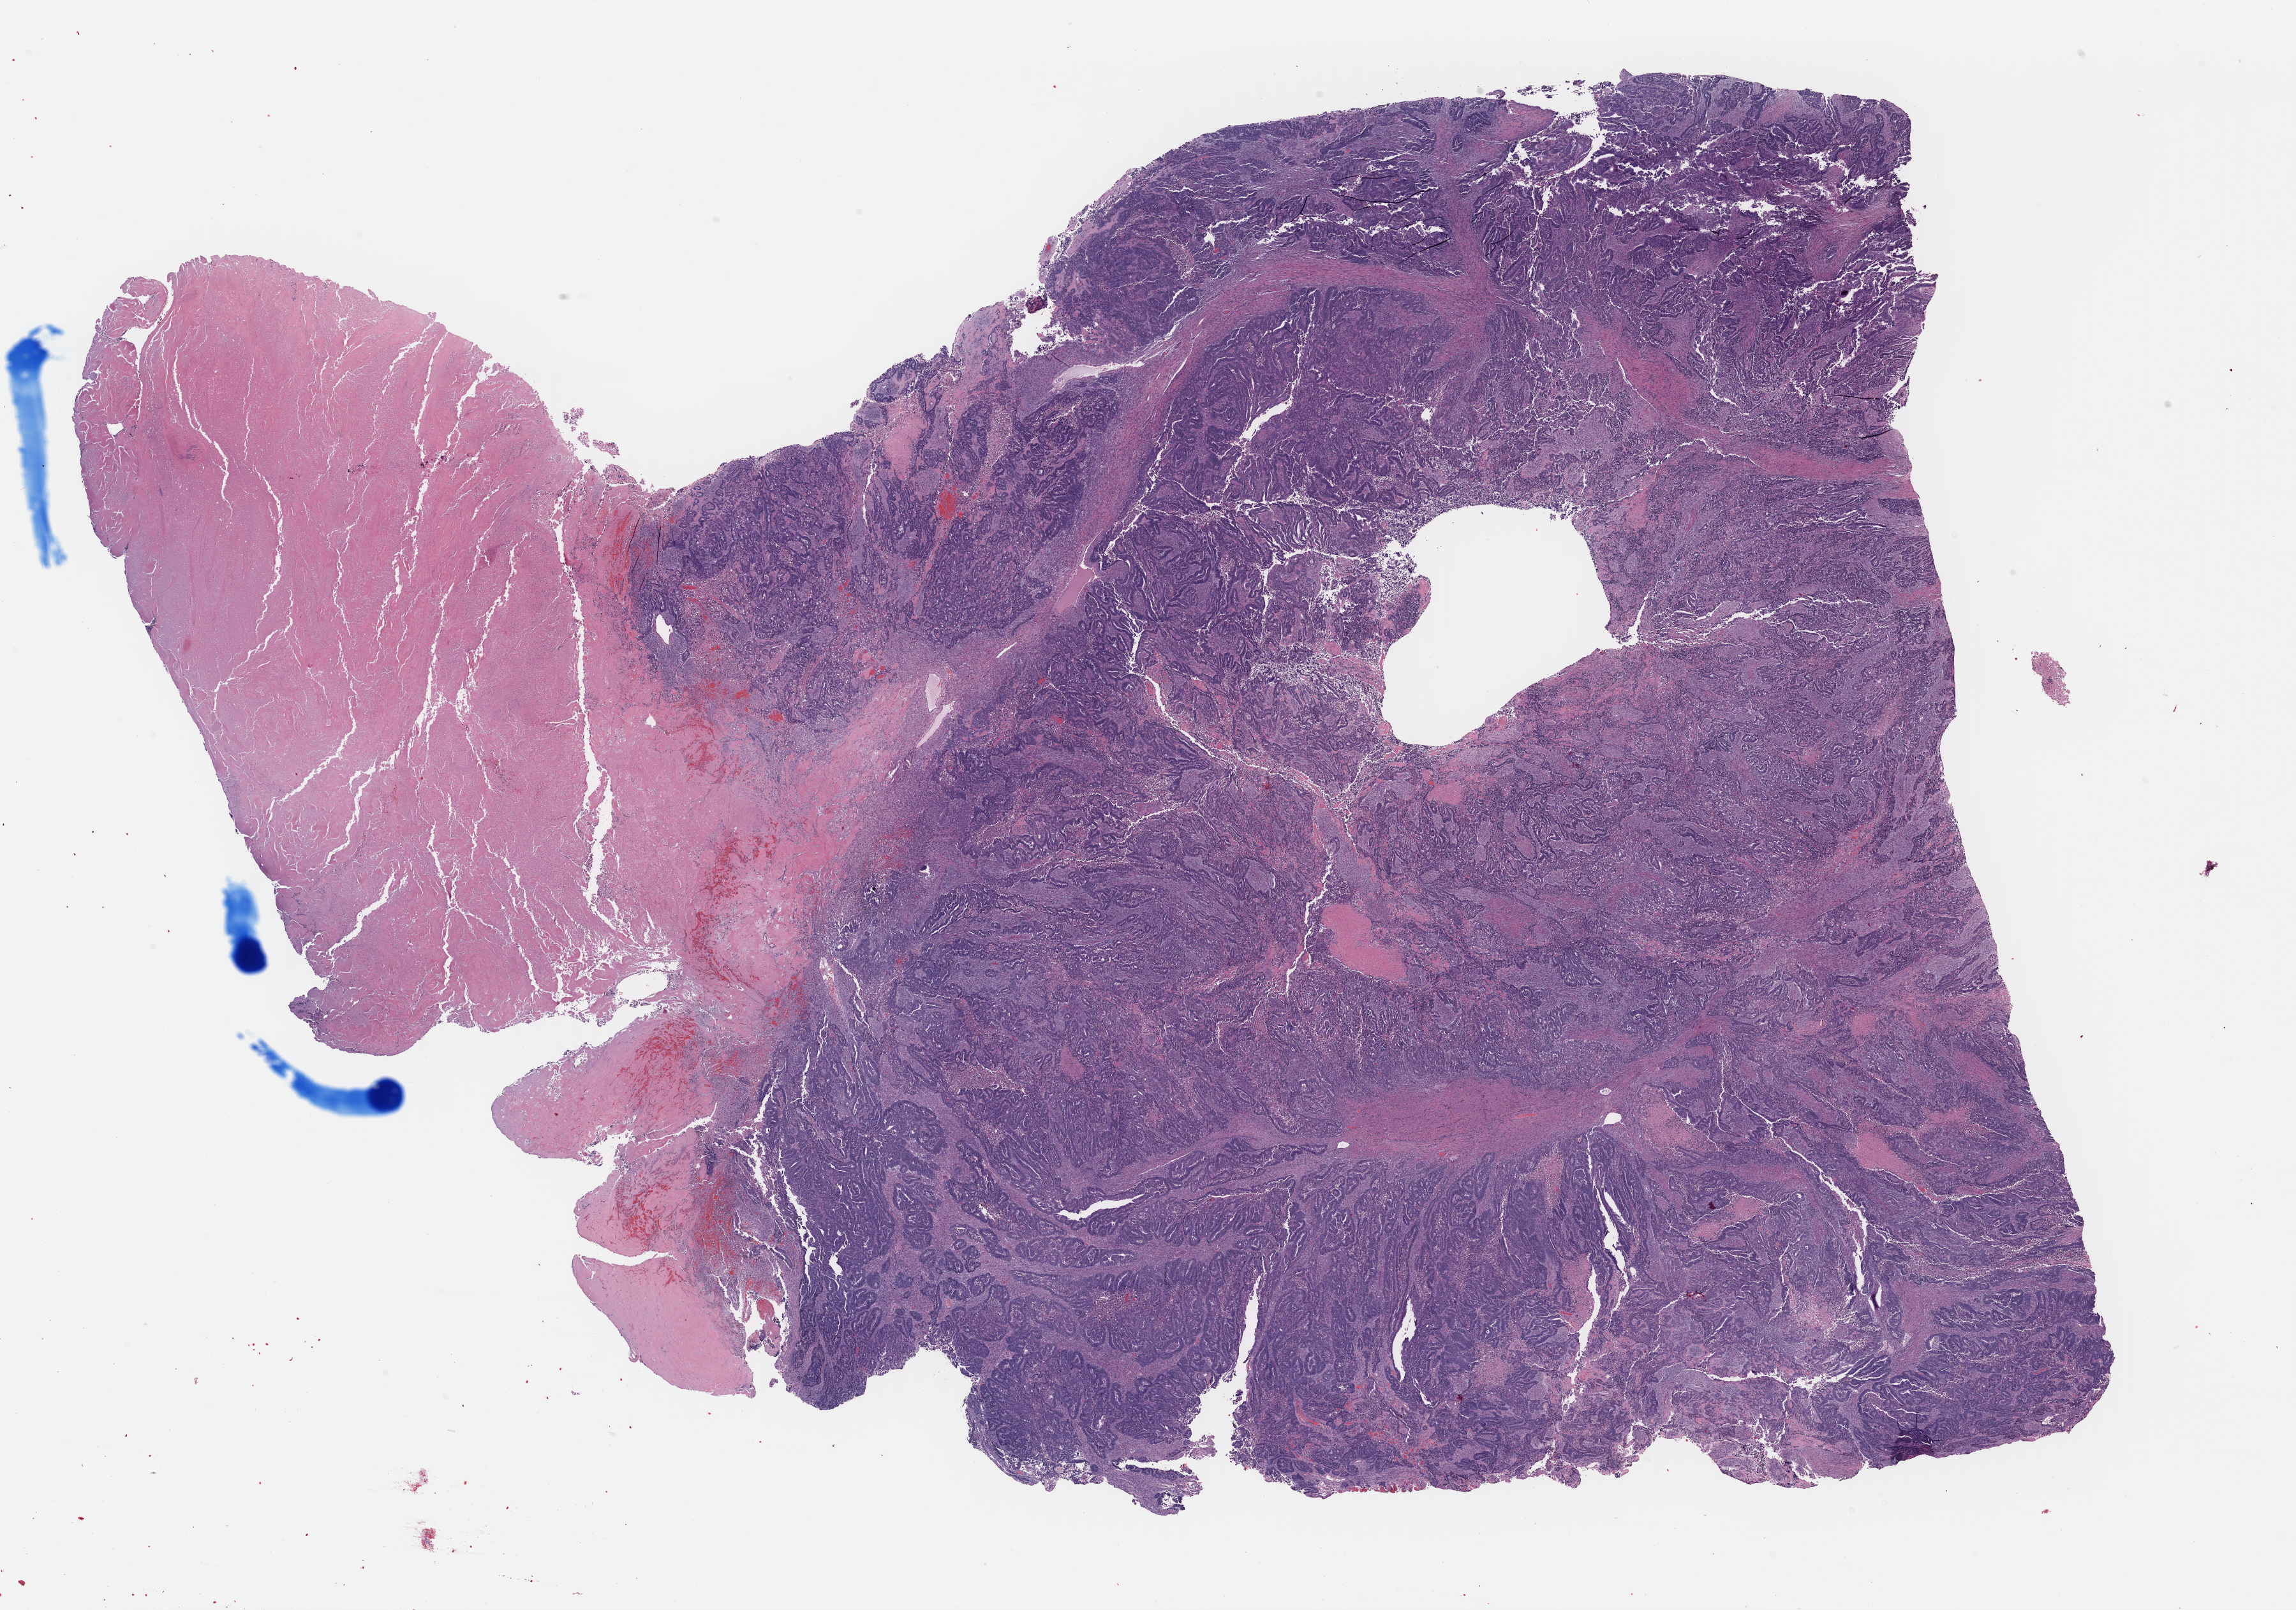
Whole-slide histology image, H&E-stained, whole scanned area (about 28.3 x 19.8 mm, slide scanned at 40x) shown as a low-resolution overview, formalin-fixed paraffin-embedded (FFPE) diagnostic section, sample: primary tumour, uterus. Female patient; age at initial diagnosis 83 years.
Diagnosis: Mullerian mixed tumor (endometrium). FIGO stage: III.